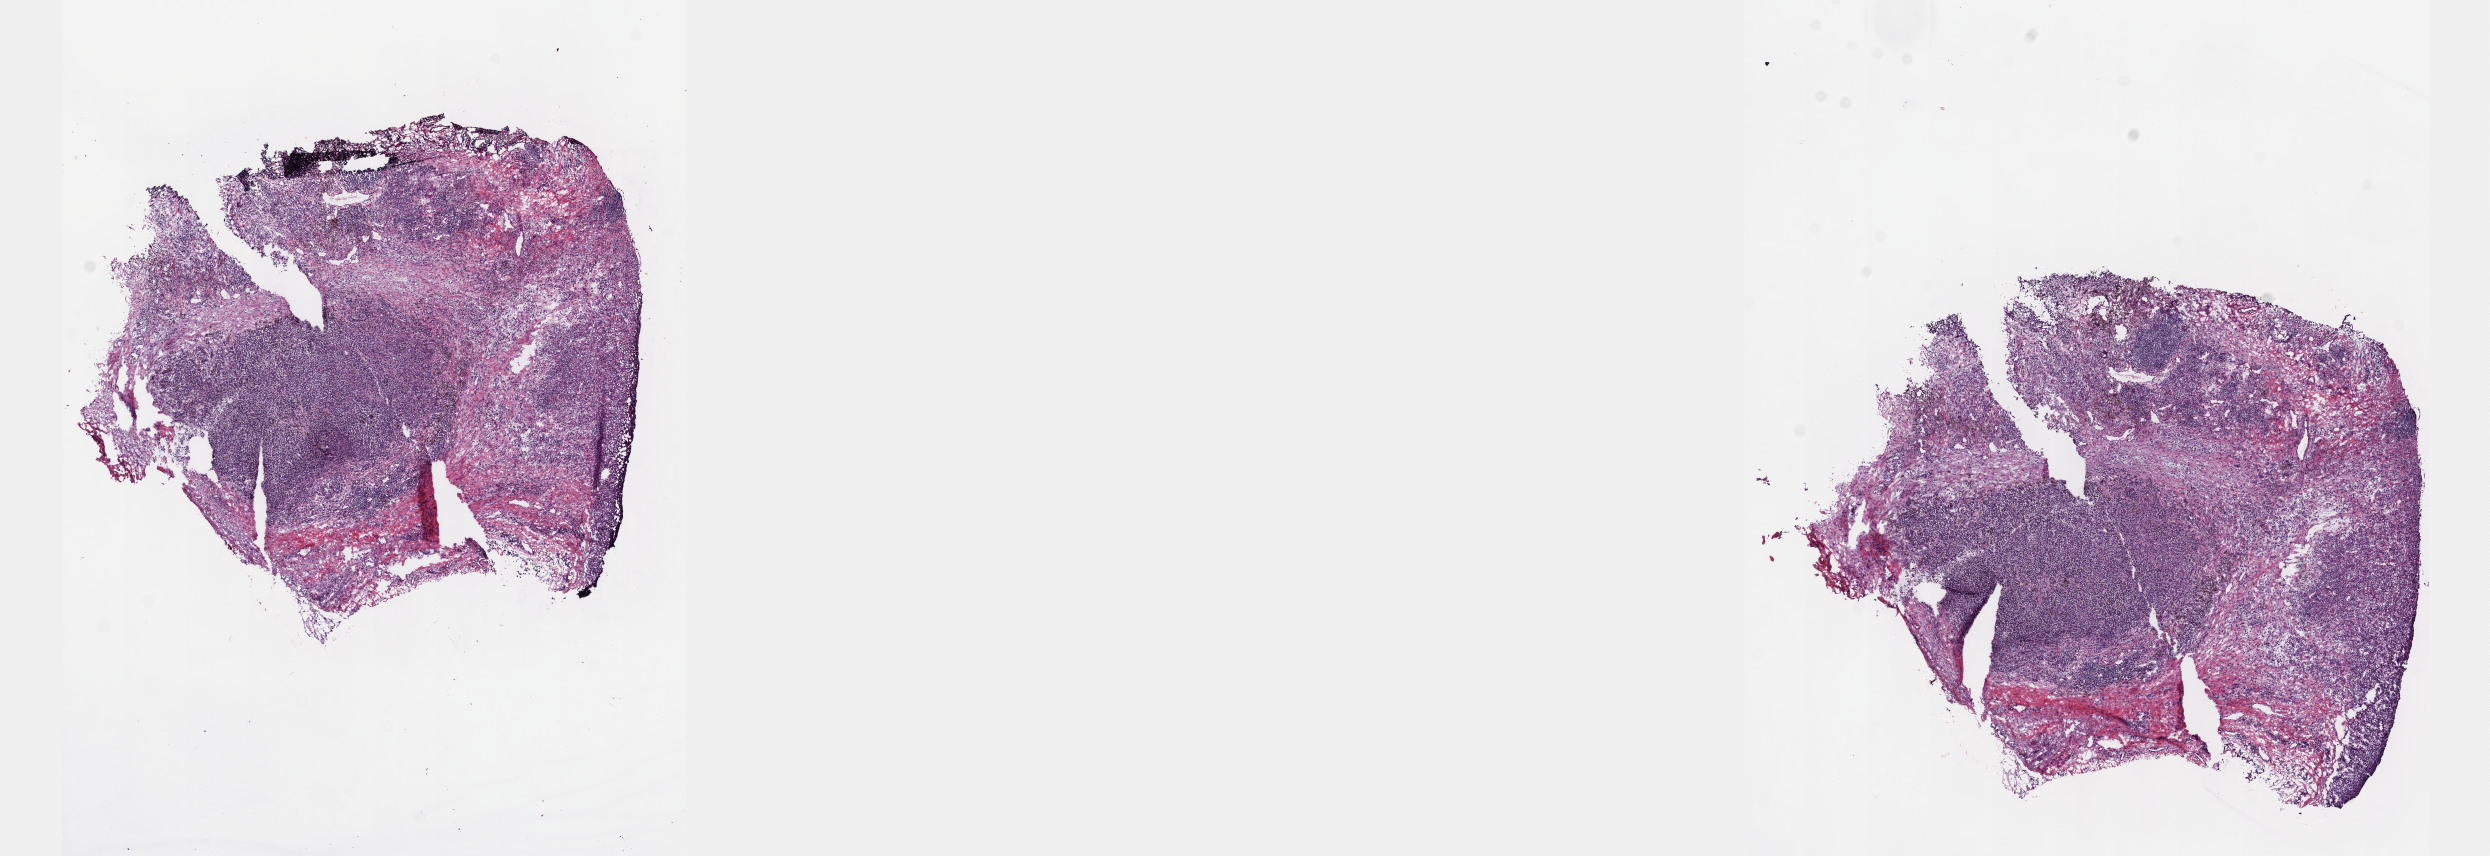
Digitized H&E-stained tissue section (whole slide) — a low-resolution overview of the entire scanned area, about 20.1 x 6.9 mm (slide scanned at 40x), frozen section from the top of the tissue portion, metastatic tumour sample, sampled site: lymph nodes of axilla or arm. Patient: female, age at initial diagnosis 54 years. Pathologist review of this section (percent, as recorded): tumour cells 100%, tumour nuclei 65%, normal cells 0%, stromal cells 0%, necrosis 0%. Inflammatory infiltration, as recorded: lymphocyte infiltration 3%, monocyte infiltration 0%, neutrophil infiltration 0%.
• this section: metastatic tumour tissue
• patient diagnosis: Malignant melanoma, NOS